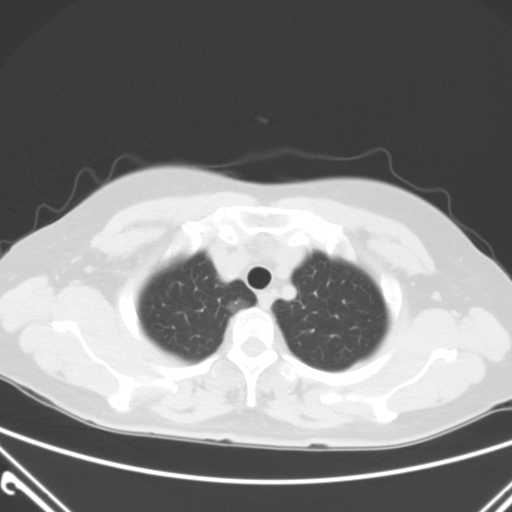
Chest CT, one axial slice; slice 49 of 60 in the series (ordered by position); 120 kVp; lung window (W 1500 / L -600 HU); 5 mm slice thickness; 512 × 512 image matrix, field of view 350 × 350 mm. Patient: female, 54 years. From the clinical record (not read from this slice): clinical TNM (as recorded): T1a N0 M0; histopathological grade: G1.
Outlined on this slice (bounding box drawn by a radiologist):
- lung tumour (recorded histology: adenocarcinoma): bounding box [x1, y1, x2, y2] px = [224, 295, 251, 318]